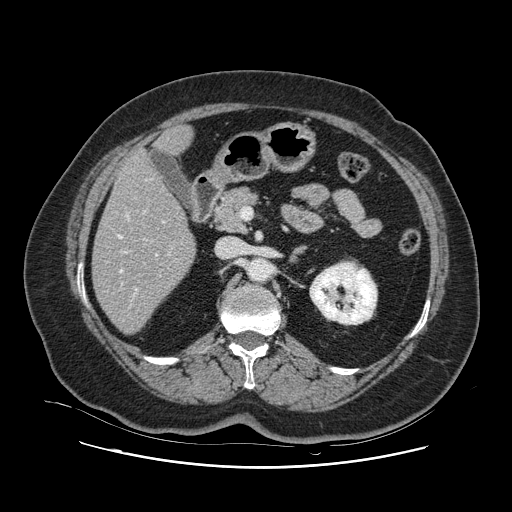
Contrast-enhanced abdominal CT, one axial slice; slice 48 of 132 in the series (ordered by position); 120 kVp; intravenous contrast given; soft-tissue window (W 400 / L 40 HU); 2.5 mm slice thickness; 512 × 512 image matrix, field of view 391 × 391 mm. Female patient, age 73 years. From the clinical record (not read from this slice): diagnosis: colorectal cancer liver metastases, imaged before liver resection; multiple liver metastases: no.
Annotated regions visible in this slice (expert manual segmentation):
- hepatic veins: bounding box [x1, y1, x2, y2] px = [118, 179, 169, 285]
- liver: [94, 127, 196, 333]
- planned liver remnant (the part of the liver to remain after resection): [94, 154, 196, 334]
- portal vein (with intrahepatic branches): [134, 221, 165, 296]